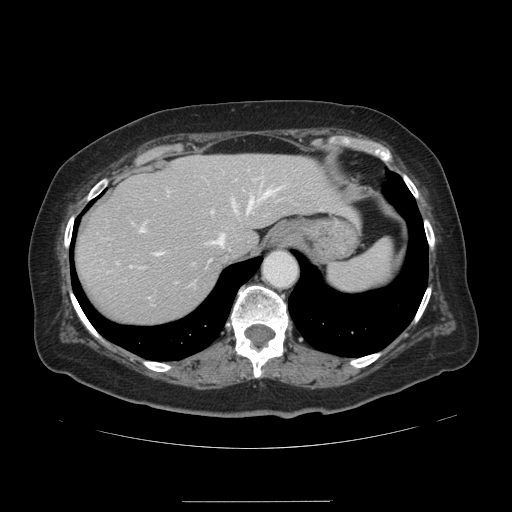
Contrast-enhanced abdominal CT, one axial slice. Position 107 of 141 along the scan axis. Intravenous contrast given. Soft-tissue window (W 400 / L 40 HU). 2.5 mm slice thickness. 512 × 512 image matrix. Female patient, age 74 years. From the clinical record (not read from this slice): diagnosis: colorectal cancer liver metastases, imaged before liver resection; multiple liver metastases: yes; largest metastasis: 7 cm; disease in both lobes: yes.
Structures marked on this image (expert manual segmentation):
- hepatic veins: bounding box (x1, y1, x2, y2) in pixels: (153, 188, 276, 261)
- liver: (75, 154, 350, 324)
- planned liver remnant (the part of the liver to remain after resection): (75, 154, 350, 324)
- portal vein (with intrahepatic branches): (129, 204, 251, 268)